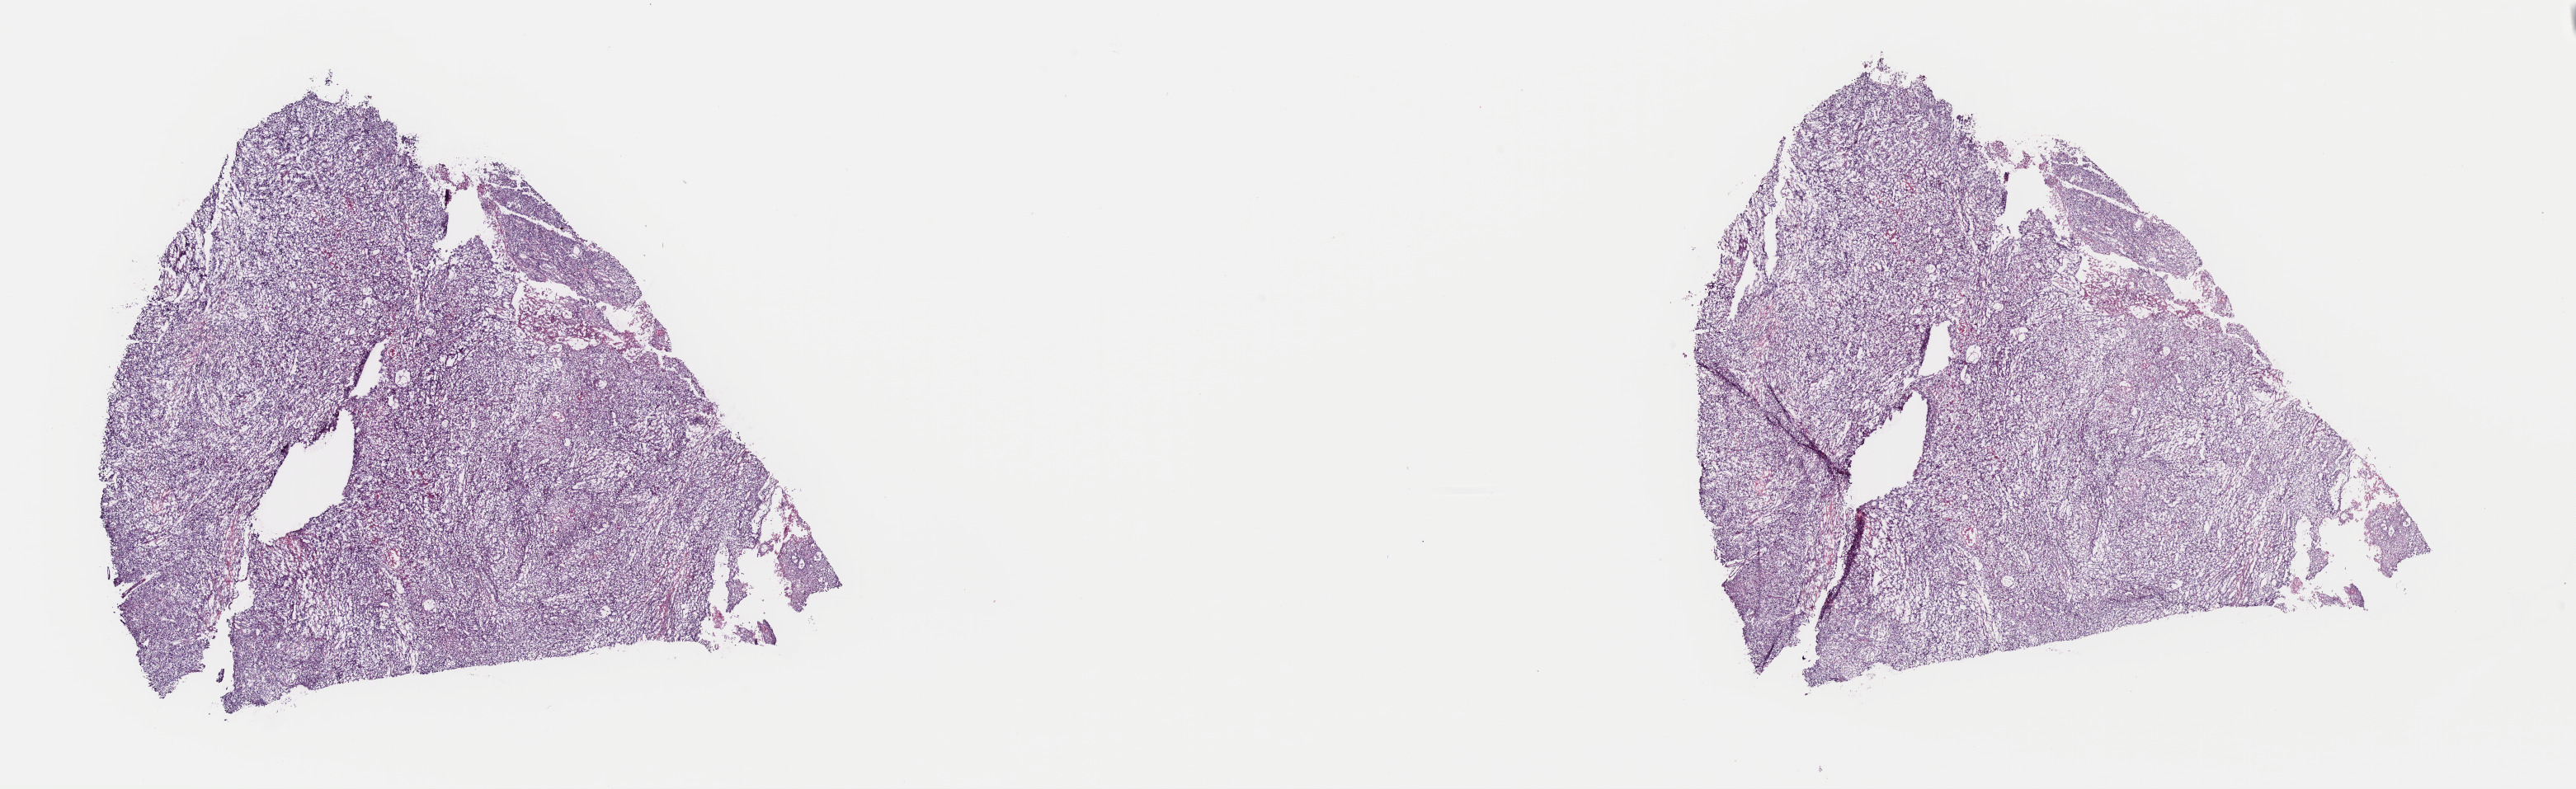
Hematoxylin and eosin (H&E) stained whole-slide image, whole scanned area (about 24.7 x 7.6 mm, acquisition: 40x scan) shown as a low-resolution overview, frozen section, bladder, primary tumour sample. Patient: male, age at initial diagnosis 74 years. Histologic grade: high grade. Pathologist review of this section (percent, as recorded): tumour cells 70%, tumour nuclei 70%, normal cells 0%, stromal cells 27%, necrosis 3%. Infiltration values recorded for this section: lymphocyte infiltration 7%, monocyte infiltration 2%, neutrophil infiltration 3%.
• AJCC pathologic stage: III (7th edition)
• diagnosis: Papillary transitional cell carcinoma (posterior wall of bladder)
• TNM: T3a N0 M0